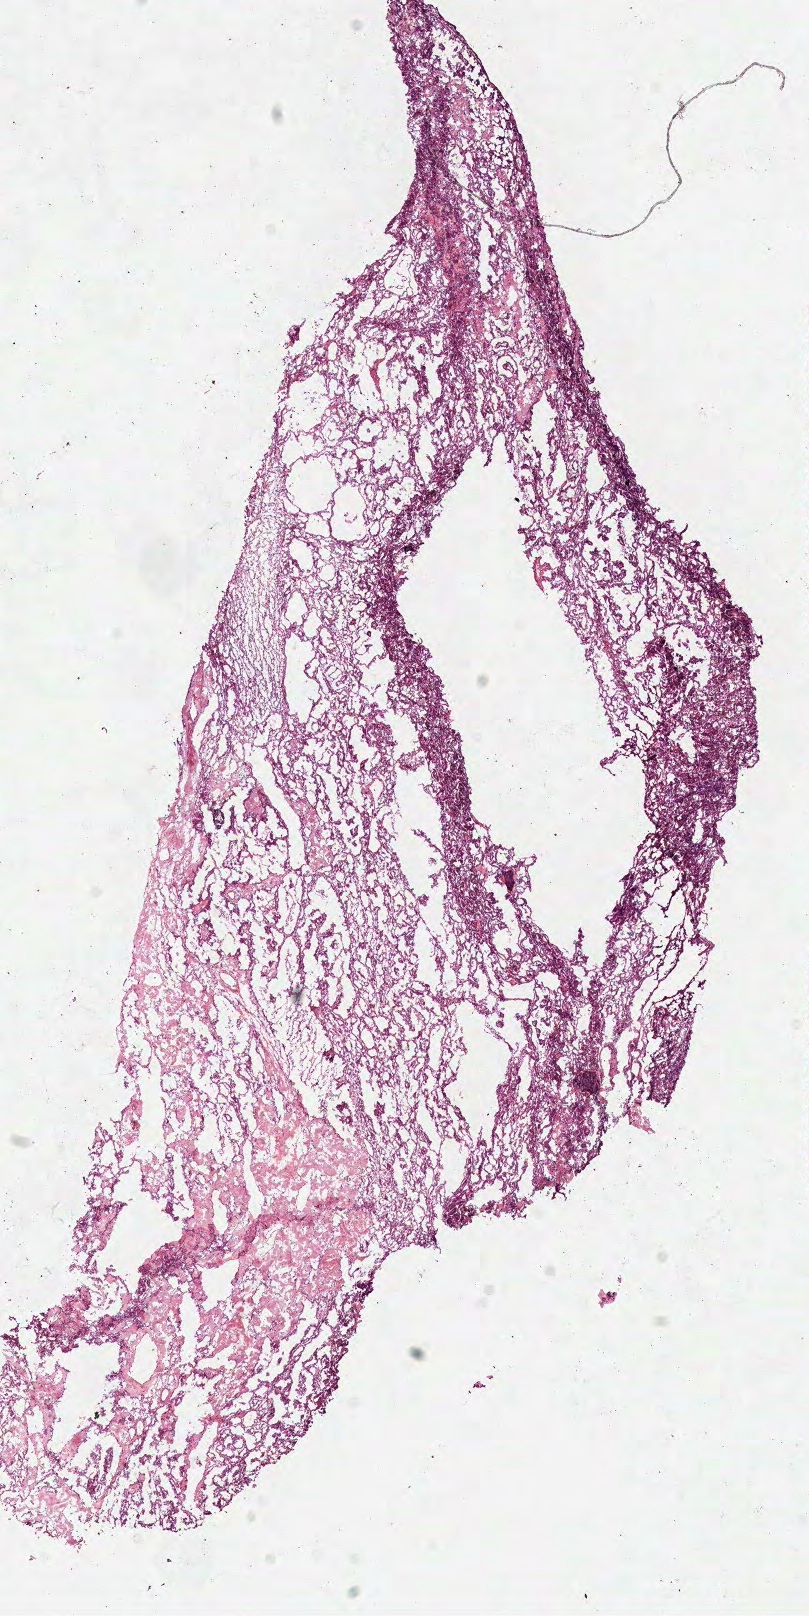
H&E-stained whole-slide image, whole scanned area (about 6.4 x 12.7 mm) shown as a low-resolution overview, frozen section from the top of the tissue portion, sample: primary tumour, kidney. Male, age 58 years at initial diagnosis. Composition of this section per pathologist review: tumour cells 75%, tumour nuclei 75%, normal cells 0%, stromal cells 25%, necrosis 0%.
- histologic diagnosis: Papillary adenocarcinoma, NOS
- TNM: T1a NX MX
- laterality: left
- AJCC pathologic stage: I